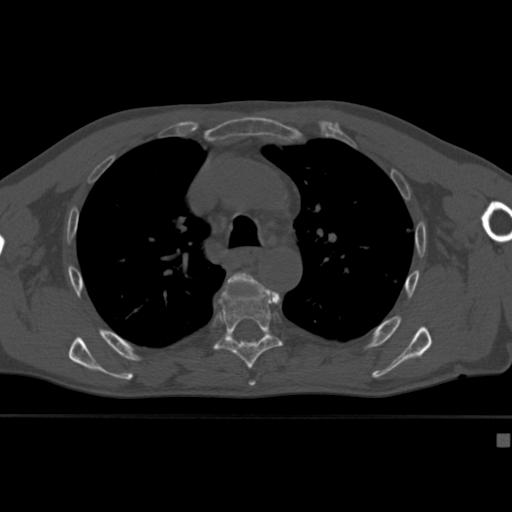
CT including the spine, one axial slice. Position 296 of 430 along the scan axis. 120 kVp. Bone window (W 1800 / L 400 HU). 1.5 mm slice thickness. 512 × 512 image matrix, field of view 337 × 337 mm. Male patient, age 64 years. From the clinical record (not read from this slice): primary cancer: uterus; vertebrae with lytic lesions (as recorded): T1, T4, T5, T7, L5.
Annotated regions visible in this slice (semi-automatic segmentation, software-assisted and operator-edited):
- T5 vertebra: bounding box (x1, y1, x2, y2) in pixels: (229, 272, 267, 382)
- T6 vertebra: (214, 282, 283, 370)